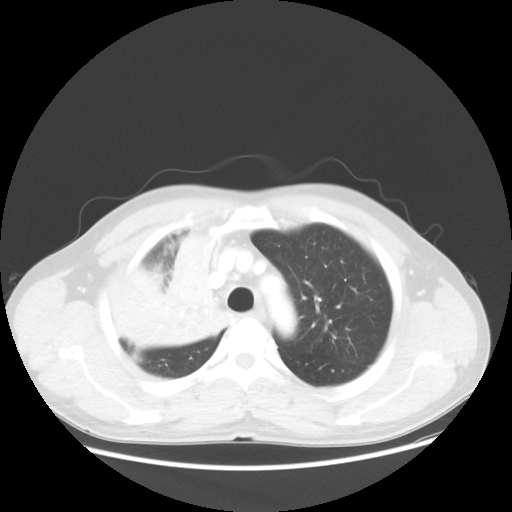
Chest CT, one axial slice; slice 42 of 56 in the series (ordered by position); lung window (W 1500 / L -600 HU); 5 mm slice thickness; 512 × 512 image matrix. Patient: male, 60 years. Case-level facts recorded for this patient, not image findings: clinical TNM (as recorded): T2a N1 M0.
Annotated regions visible in this slice (rectangle marked by the reading radiologist):
- lung tumour (recorded histology: squamous cell carcinoma): bounding box (x1, y1, x2, y2) in pixels: (142, 219, 249, 362)